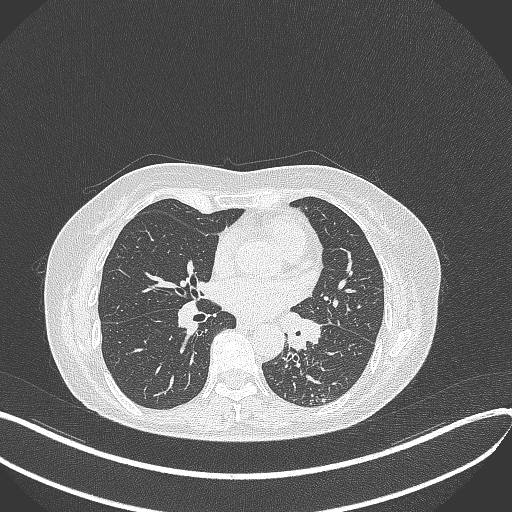
Chest CT, one axial slice; slice 201 of 429 in the series (ordered by position); reconstruction kernel B70f; 100 kVp; lung window (W 1500 / L -600 HU); 1 mm slice thickness; 512 × 512 image matrix. Female patient, age 63 years. Case-level facts recorded for this patient, not image findings: clinical TNM (as recorded): T1b N0 M0; histopathological grade: G2-3.
Outlined on this slice (bounding box drawn by a radiologist):
- lung tumour (recorded histology: adenocarcinoma): bounding box [x1, y1, x2, y2] px = [281, 312, 325, 353]